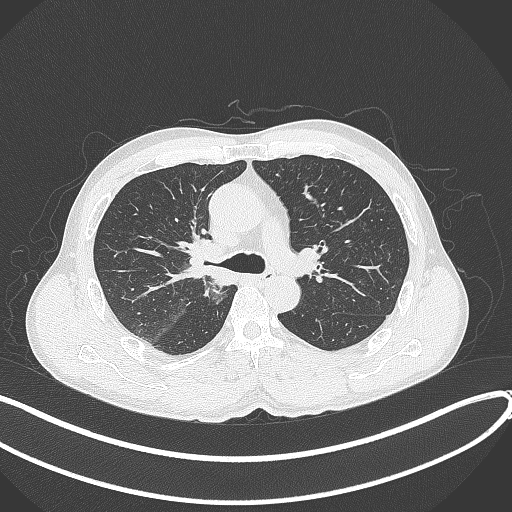
Chest CT, one axial slice; position 252 of 409 along the scan axis; lung window (W 1500 / L -600 HU); 1 mm slice thickness; 512 × 512 image matrix. Male patient, age 53 years. Case-level facts recorded for this patient, not image findings: clinical TNM (as recorded): T1b N0 M0.
Structures marked on this image (rectangle marked by the reading radiologist):
- lung tumour (recorded histology: squamous cell carcinoma): box from (x=177, y=235) to (x=227, y=280) px